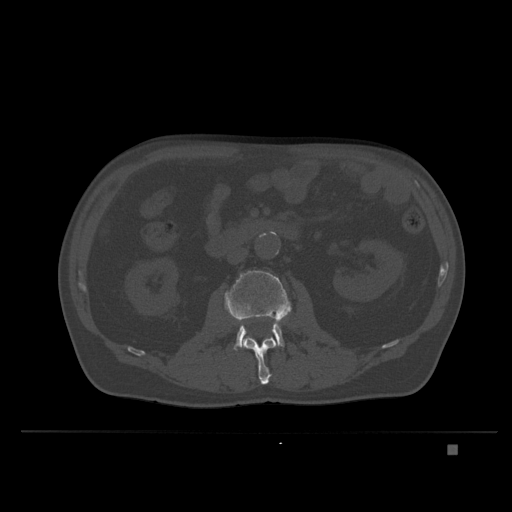
CT including the spine, one axial slice. Slice 107 of 435 in the series (ordered by position). Bone window (W 1800 / L 400 HU). 512 × 512 image matrix. Patient: male, 73 years. Case-level facts recorded for this patient, not image findings: primary cancer: skin.
Structures marked on this image (semi-automatic segmentation, software-assisted and operator-edited):
- L2 vertebra: bounding box [x1, y1, x2, y2] px = [242, 336, 277, 385]
- L3 vertebra: [224, 270, 292, 350]